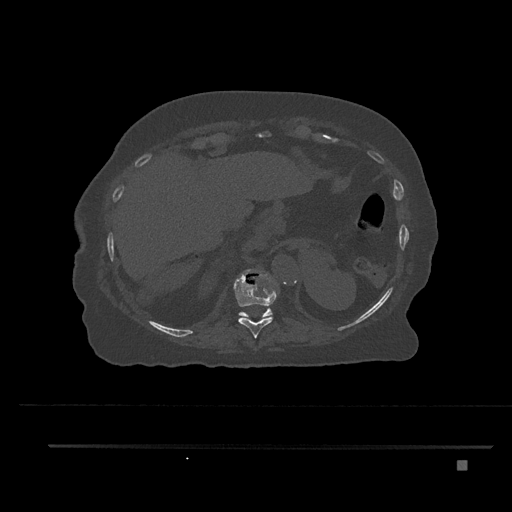
CT including the spine, one axial slice. Slice 343 of 797 in the series (ordered by position). Reconstruction kernel Br40s/3. Bone window (W 1800 / L 400 HU). 0.5 mm slice thickness. 512 × 512 image matrix, field of view 437 × 437 mm. Female patient, age 76 years. From the clinical record (not read from this slice): primary cancer: lung.
Structures marked on this image (semi-automatically segmented with operator editing):
- T10 vertebra: box from (x=234, y=272) to (x=277, y=338) px
- T11 vertebra: (x=238, y=290)–(x=276, y=319)